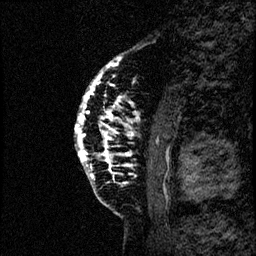
Breast MRI (dynamic contrast-enhanced), one sagittal slice; position 16 of 60 along the scan axis; dynamic contrast-enhanced study with each time point stored as its own series, time point 2 of 4 at this slice position (early post-contrast, ordered by acquisition time); 1.5 T; TE 4.2 ms, TR 17.6 ms; 2 mm slice thickness; 256 × 256 image matrix, field of view 200 × 200 mm. Female patient, age 40 years. Case-level facts recorded for this patient, not image findings: setting: breast cancer imaged before/during neoadjuvant chemotherapy; receptor status: HER2-positive.
Annotated regions visible in this slice (semi-automatic segmentation, software-assisted and operator-edited):
- analysis volume of interest (the breast-tissue region the enhancement analysis was run in; not a lesion): box from (x=71, y=55) to (x=179, y=206) px
- tumour enhancement mask (voxels above the 100 % enhancement threshold inside the analysis volume of interest): (x=74, y=58)–(x=134, y=175)